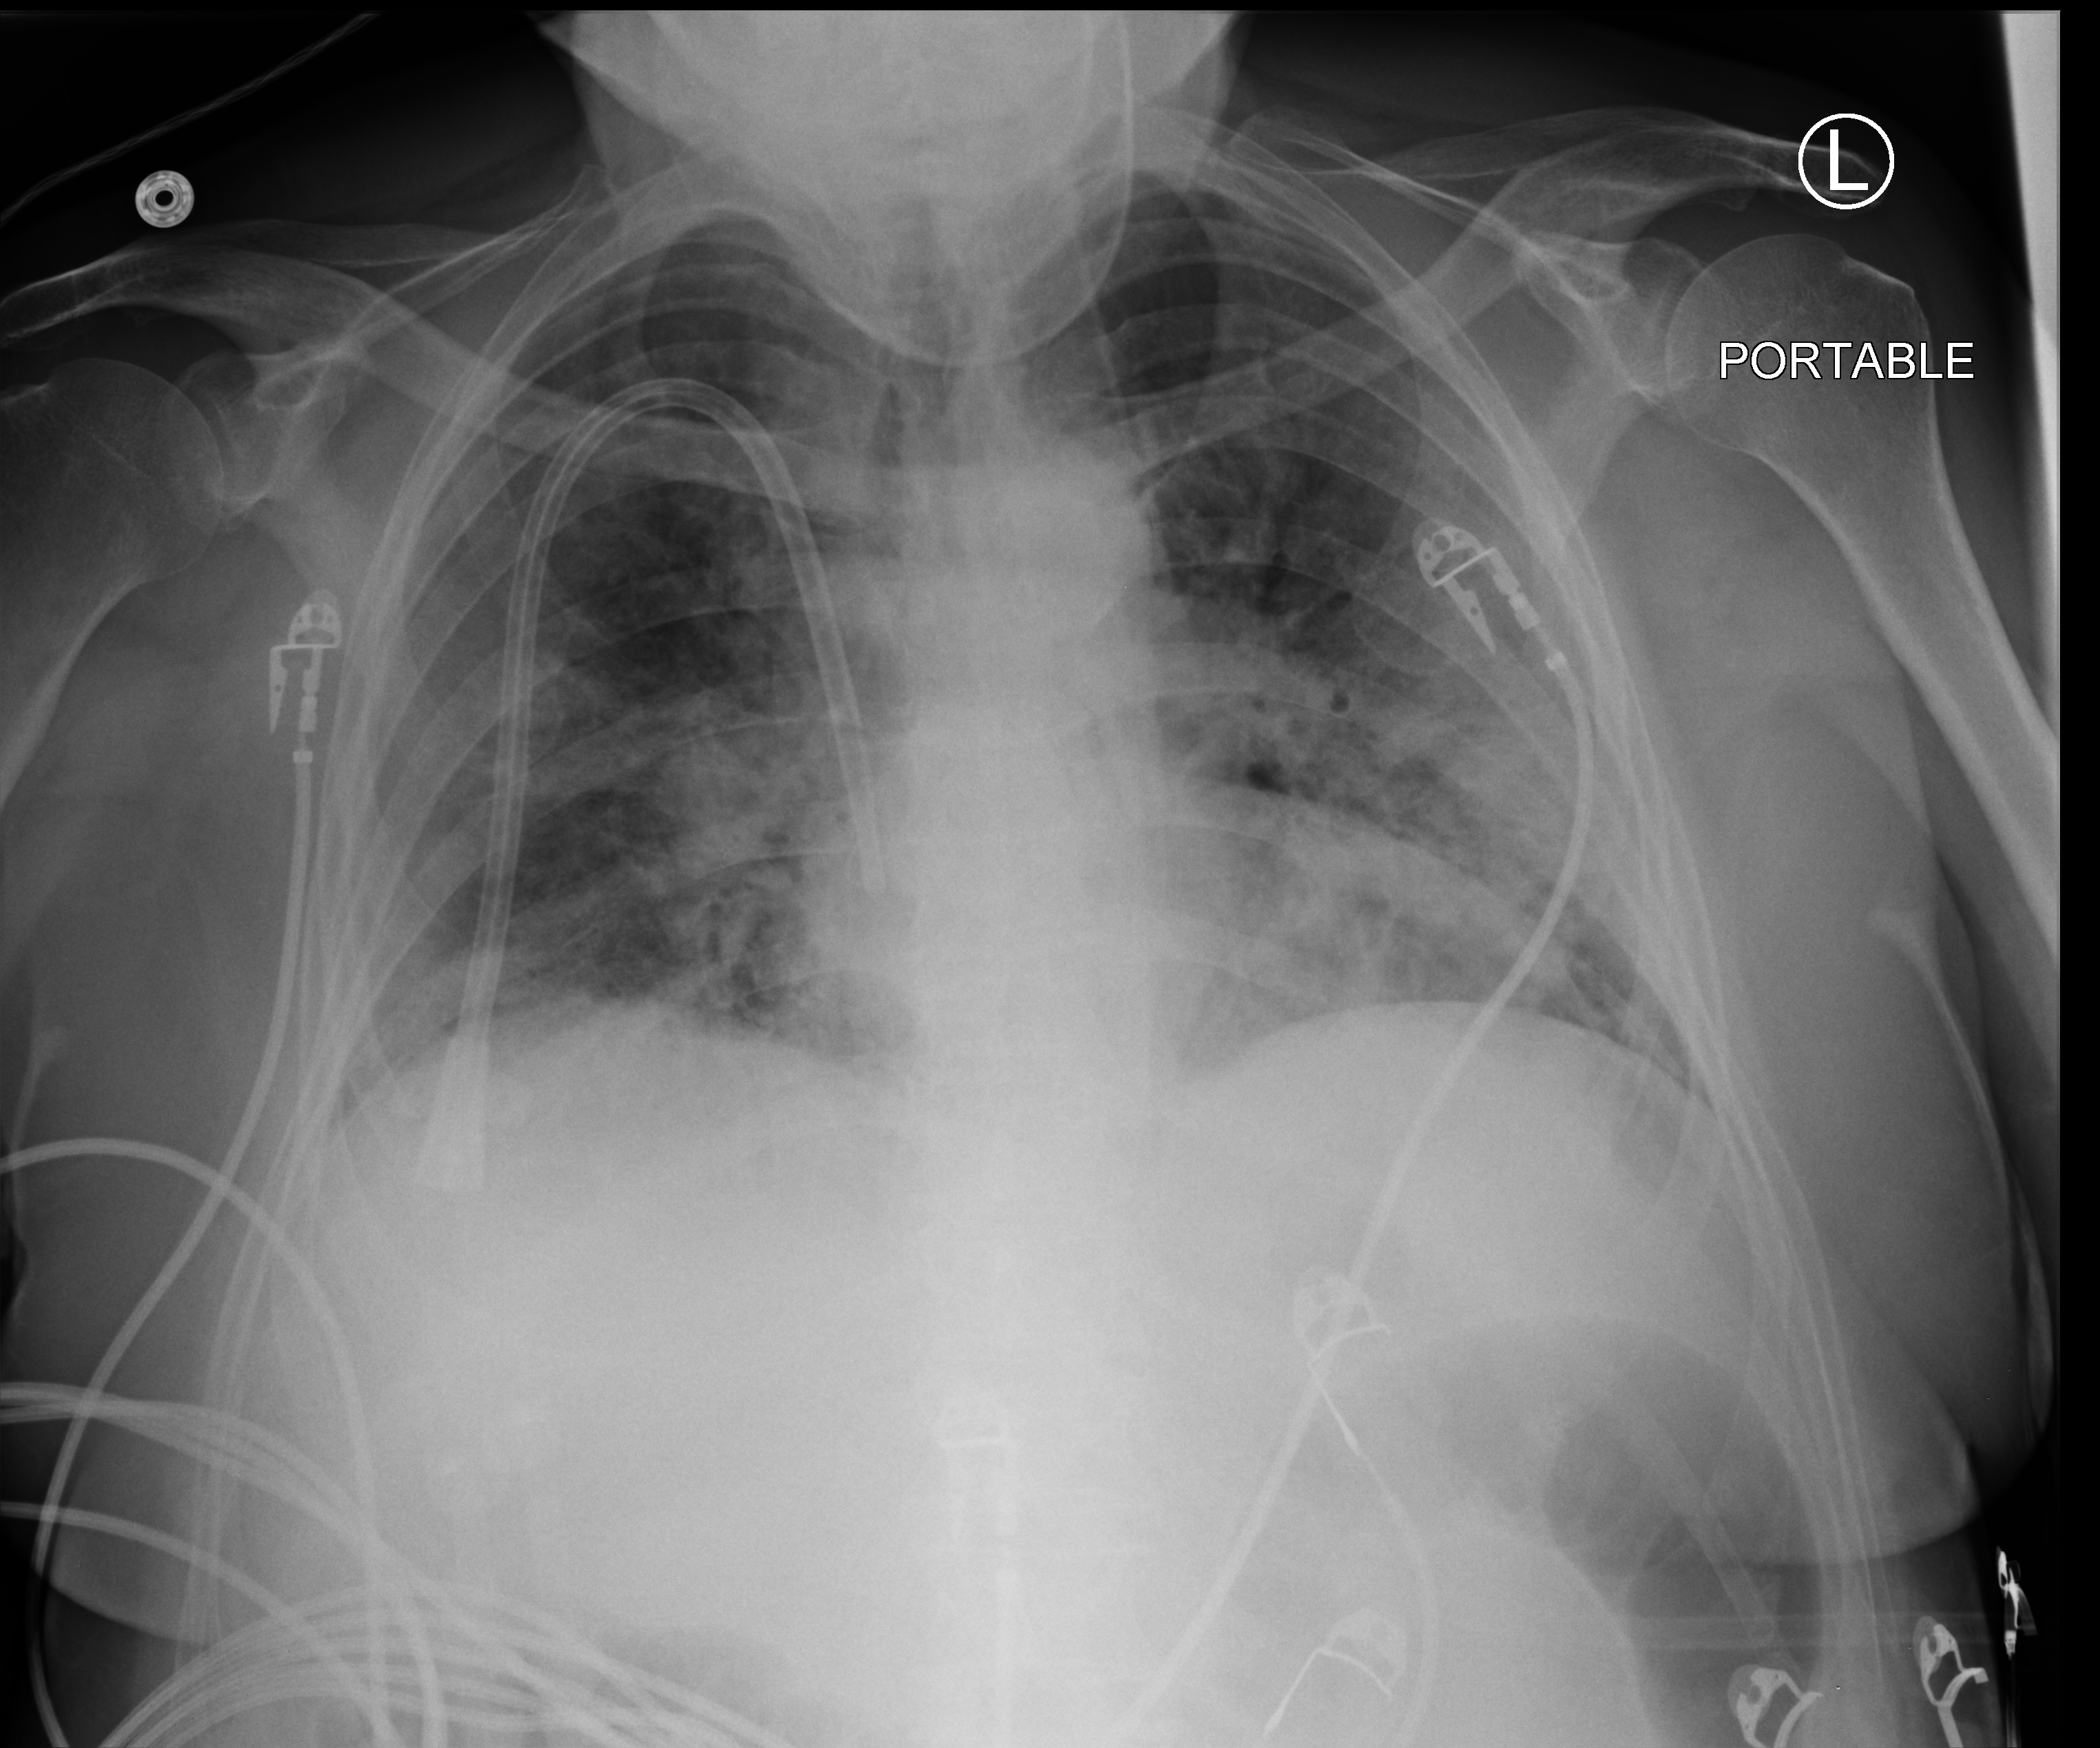
Chest X-ray (portable), anteroposterior (AP) projection. Patient hospitalised with COVID-19; male, aged 60–74 years.
Admission-level facts for this patient (not findings on this image; timing relative to this image not recorded):
- smoking status (admission record): former
- admitted to intensive care during this hospital stay: no